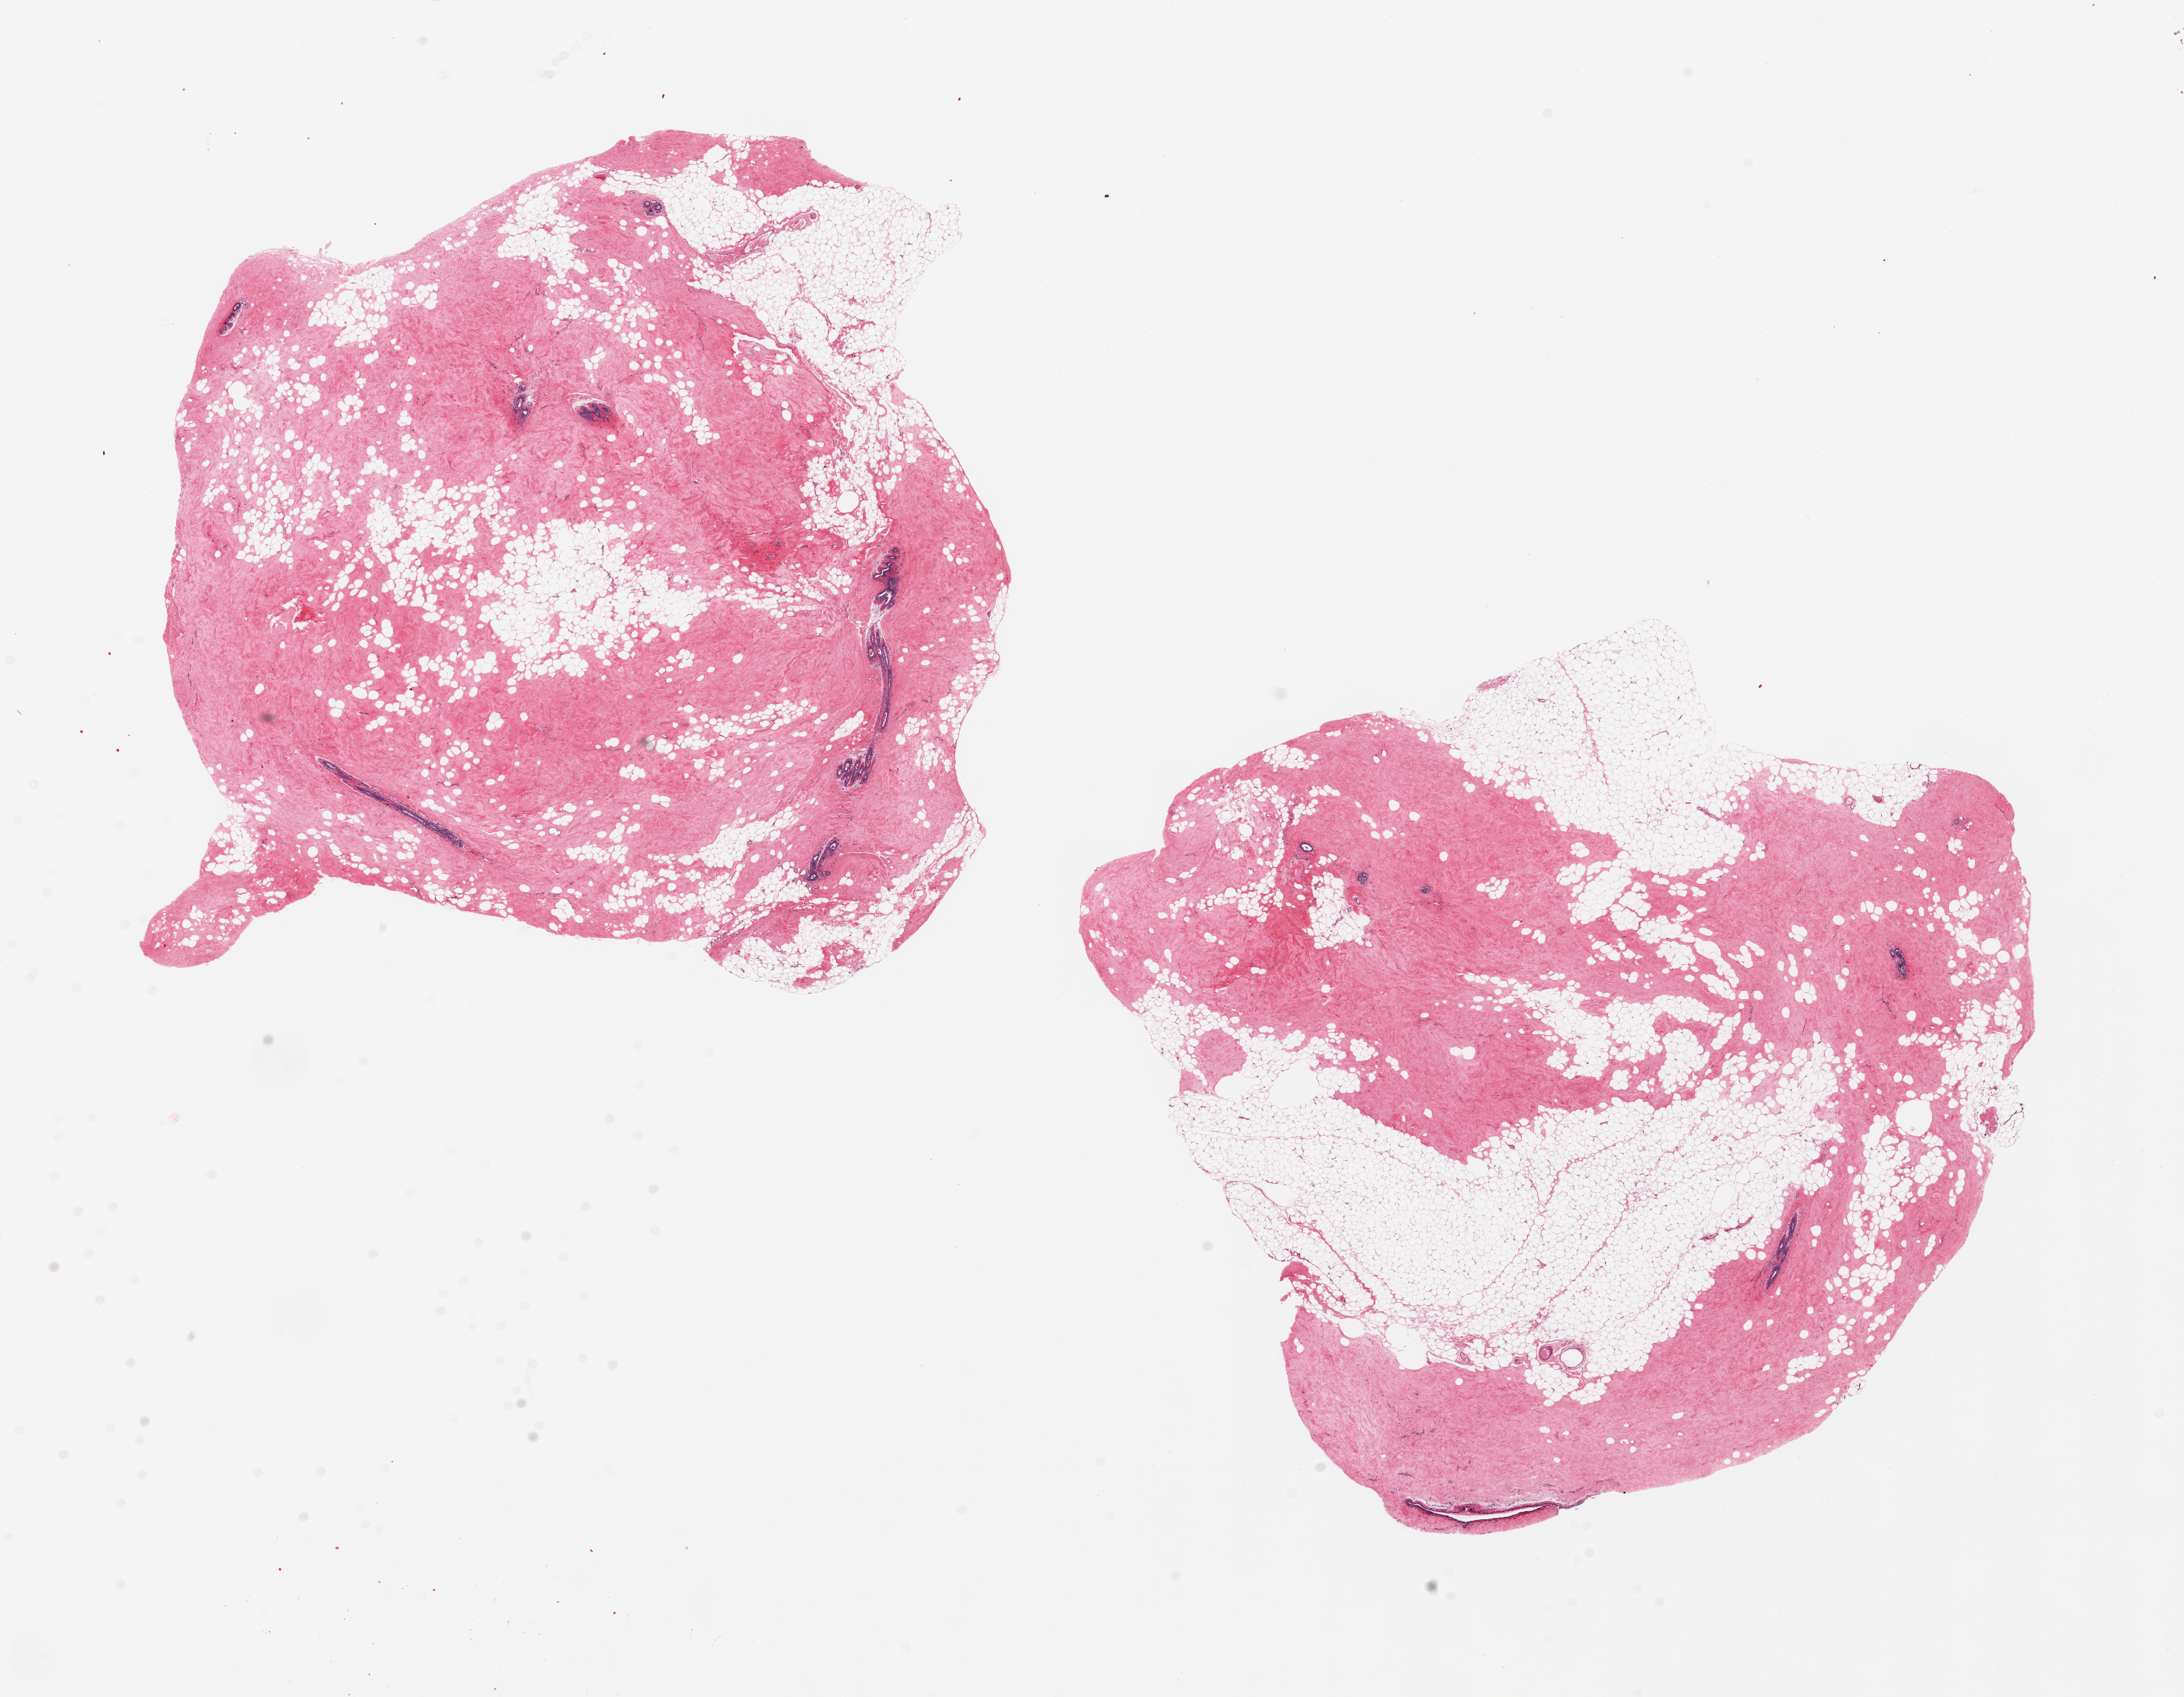
Digitized haematoxylin and eosin-stained section, brightfield — a low-resolution overview of the entire scanned area, about 22.6 x 17.6 mm (acquisition: 20x scan). PAXgene-fixed paraffin-embedded (PFPE) section. Section of breast (target tissue). Tissue donor sample. Donor sex: female.
Review note (as recorded): 2 pieces, 11x10 & 10x9mm; fibrofatty tissue with scattered atrophic lobules and ducts.